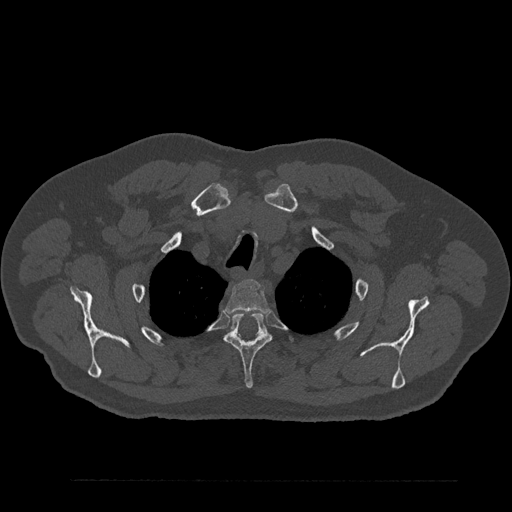
CT including the spine, one axial slice; slice 688 of 797 in the series (ordered by position); 120 kVp; bone window (W 1800 / L 400 HU); 0.5 mm slice thickness; 512 × 512 image matrix, field of view 430 × 430 mm. Patient: male, 61 years. From the clinical record (not read from this slice): primary cancer: prostate.
Annotated regions visible in this slice (semi-automatic segmentation, software-assisted and operator-edited):
- T2 vertebra: bounding box [x1, y1, x2, y2] px = [225, 279, 269, 313]
- T3 vertebra: [224, 313, 272, 389]